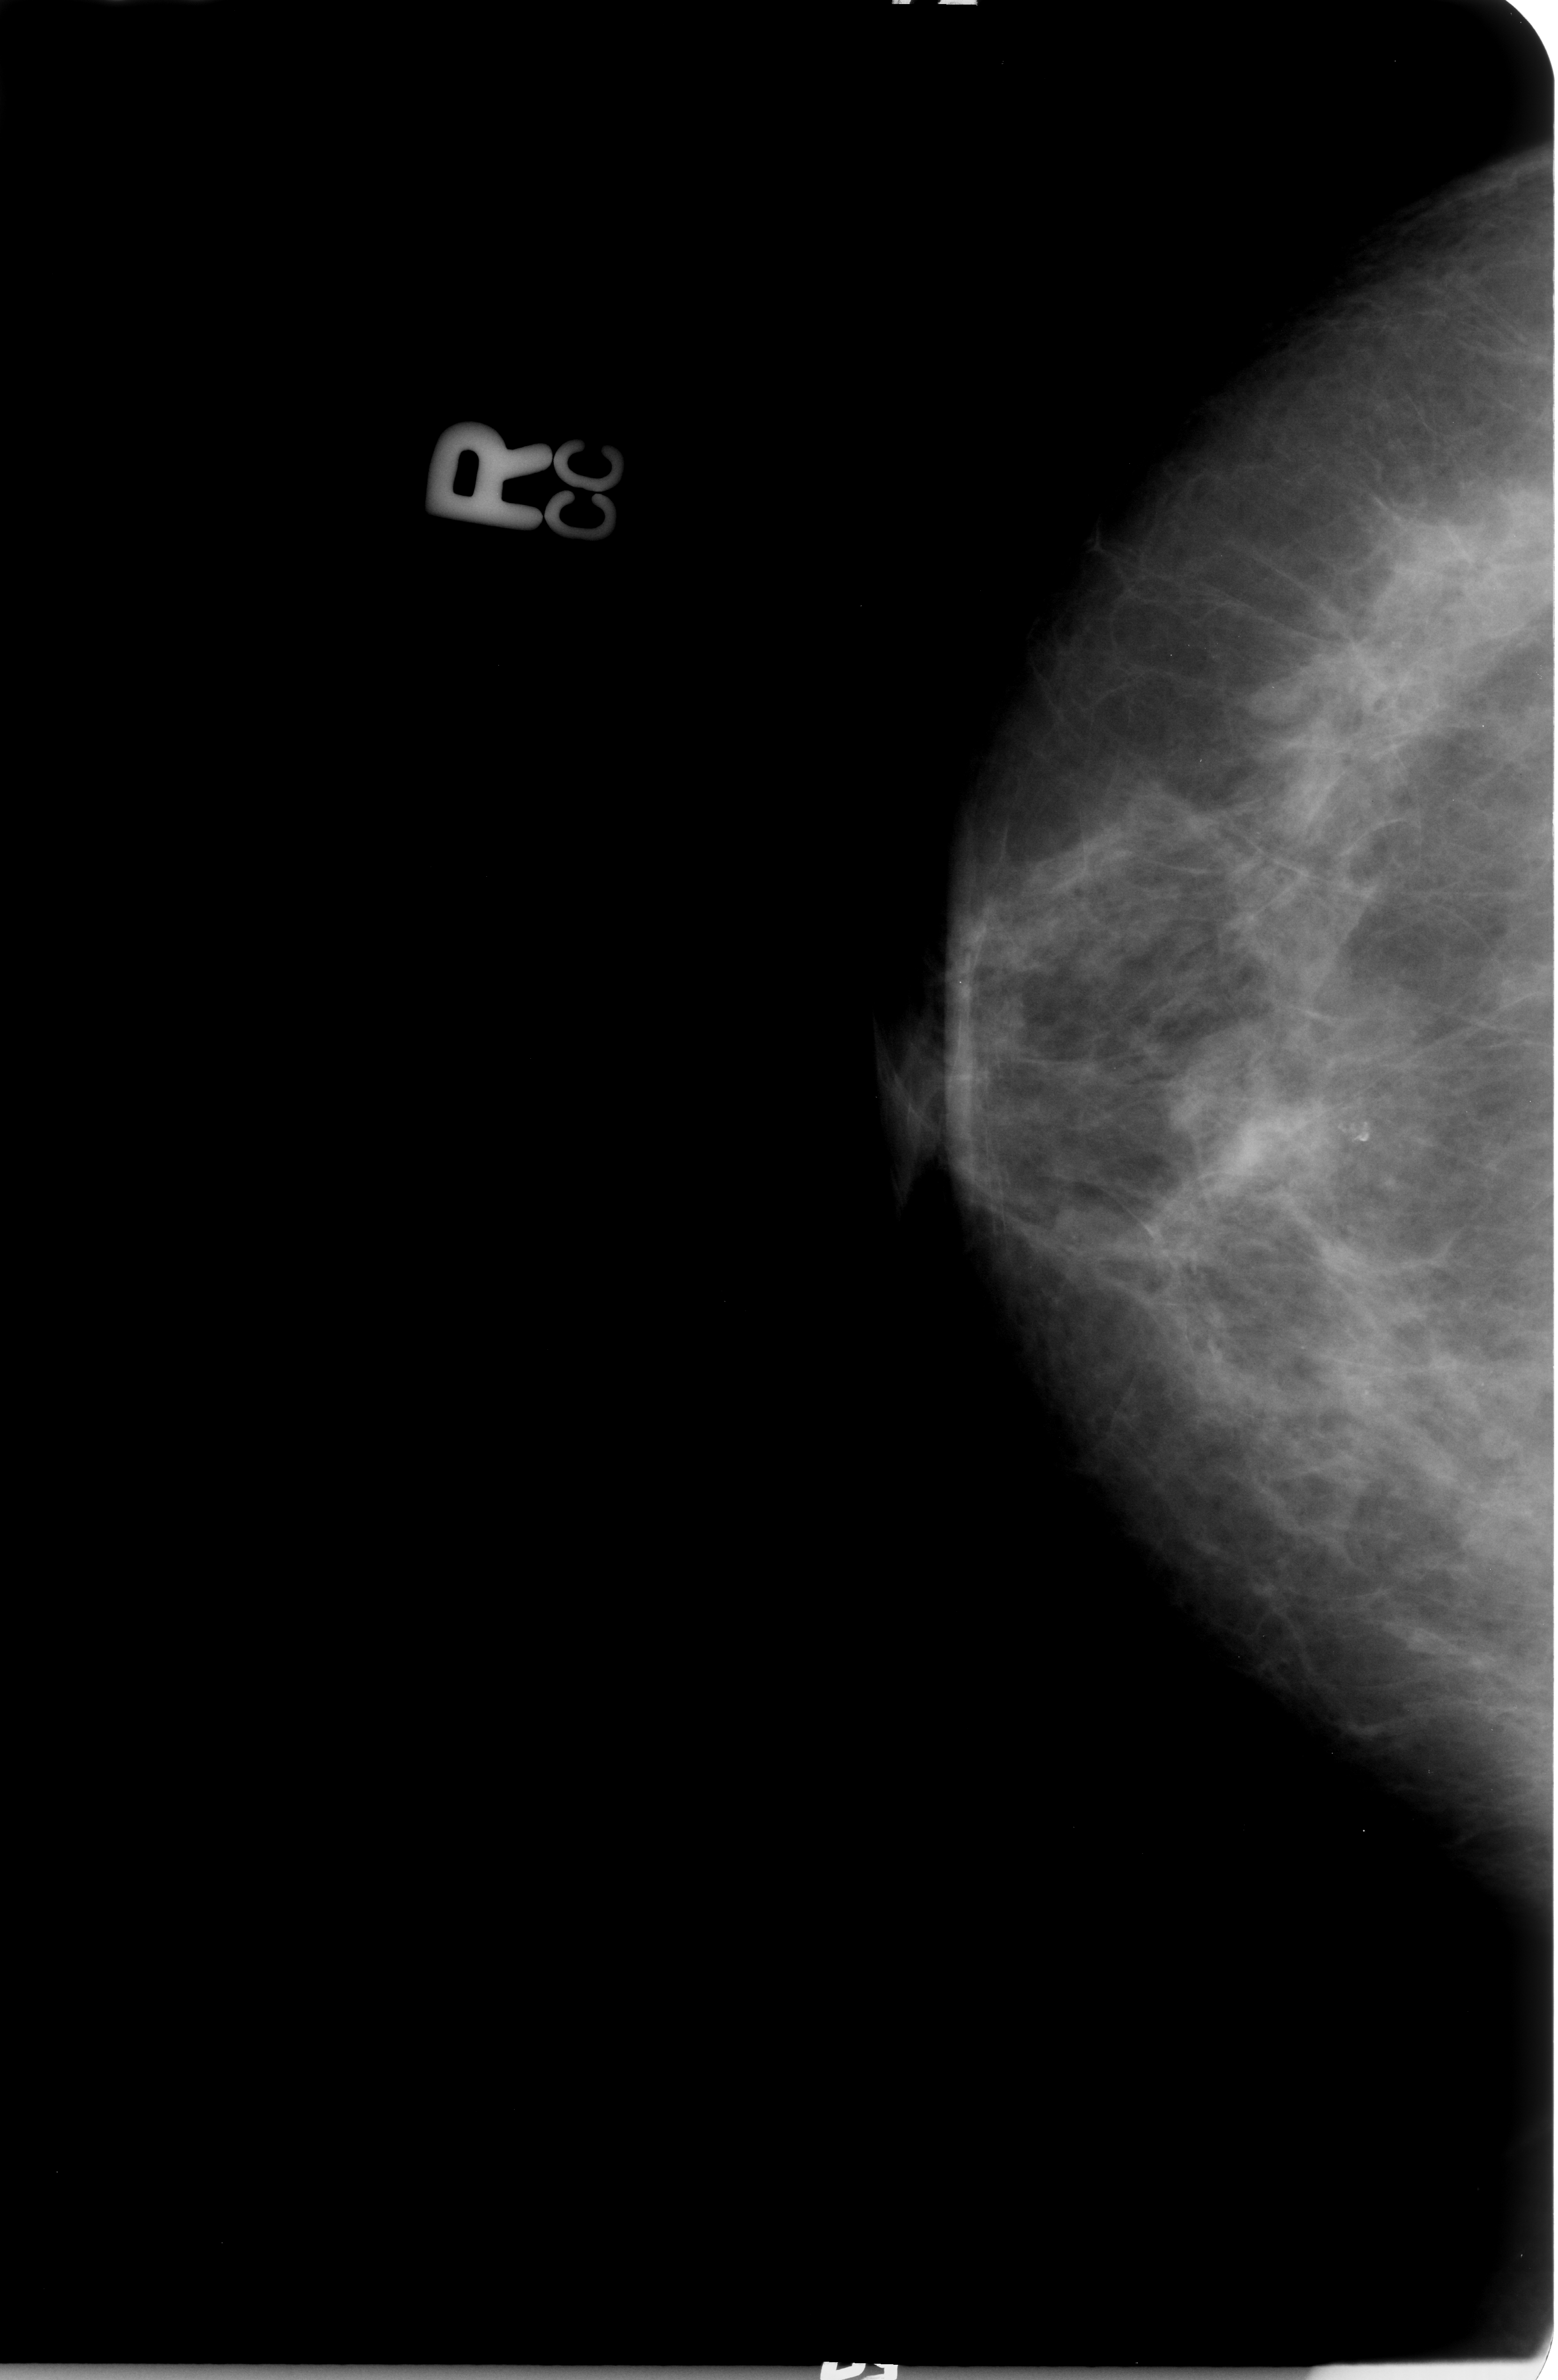
Scanned film-screen mammogram. Right breast. Craniocaudal (CC) view. 1558 × 2380 image matrix.
Marked abnormalities (boxes around the expert regions of interest):
- Finding 1 of 2: mass, shape architectural distortion; BI-RADS assessment category 2; pathology (as recorded): benign: box from (x=874, y=1046) to (x=943, y=1210) px
- Finding 2 of 2: mass, shape architectural distortion; BI-RADS assessment category 2; subtlety rating 3 on a 1 (subtle) to 5 (obvious) scale; pathology result (as recorded, not read from the image): benign: (x=925, y=916)–(x=994, y=1137)